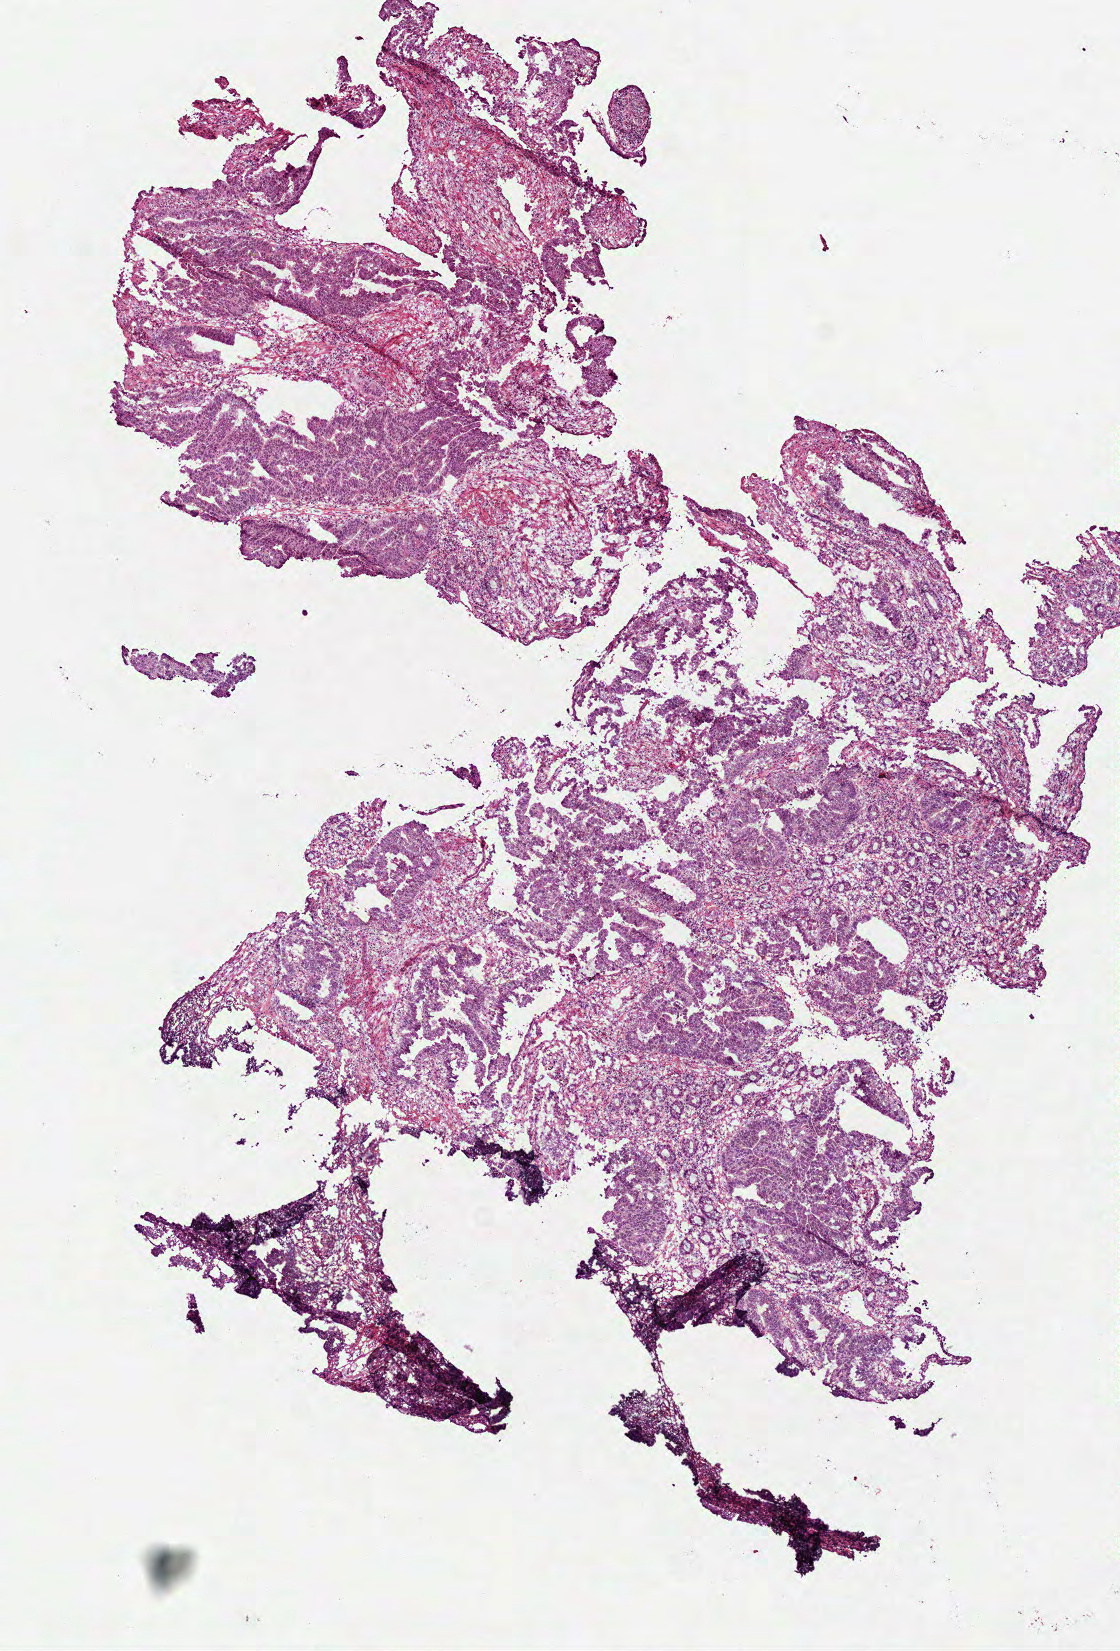
Whole-slide histology image, Hematoxylin and eosin (H&E) stained — a low-resolution overview of the entire scanned area, about 4.5 x 6.7 mm, frozen section from the top of the tissue portion, primary tumour sample from the rectum. Patient: female, age at initial diagnosis 41 years. Pathologist review of this section (percent, as recorded): tumour cells 70%, tumour nuclei 65%, normal cells 15%, stromal cells 15%, necrosis 0%.
- diagnosis: Adenocarcinoma, NOS
- TNM: T3 N1 M1
- AJCC pathologic stage: IVA (7th edition)